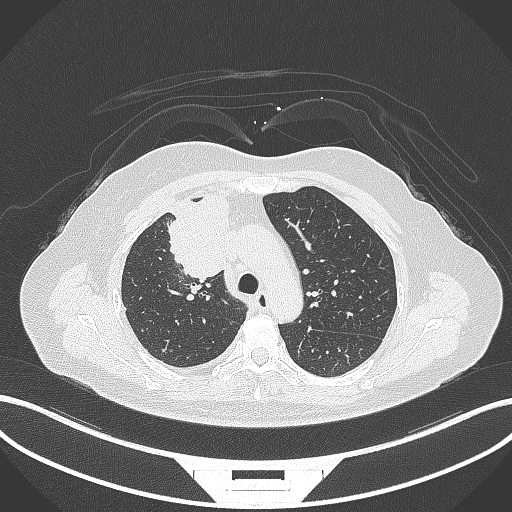
Chest CT, one axial slice; position 208 of 305 along the scan axis; reconstruction kernel B70f; 120 kVp; lung window (W 1500 / L -600 HU); 1 mm slice thickness; 512 × 512 image matrix, field of view 400 × 400 mm. Patient: female, 52 years. From the clinical record (not read from this slice): clinical TNM (as recorded): T3 N1 M1.
Outlined on this slice (rectangle marked by the reading radiologist):
- lung tumour (recorded histology: adenocarcinoma): bounding box (x1, y1, x2, y2) in pixels: (161, 189, 238, 282)